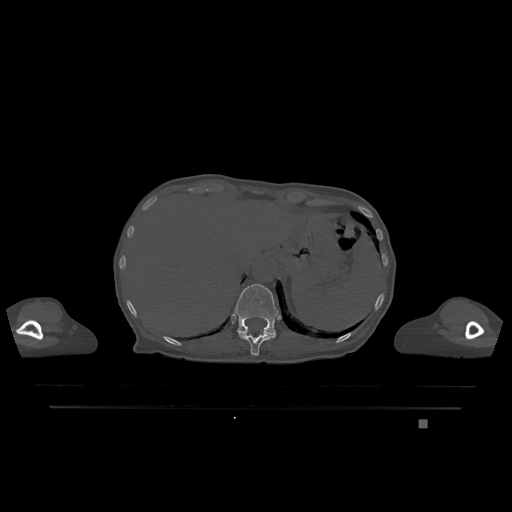
CT including the spine, one axial slice; slice 557 of 1317 in the series (ordered by position); bone window (W 1800 / L 400 HU); 0.5 mm slice thickness; 512 × 512 image matrix, field of view 500 × 500 mm. Female patient, age 74 years. Case-level facts recorded for this patient, not image findings: primary cancer: lung; vertebrae with lytic lesions (as recorded): T1, T4, T5, T6, L4, L5.
Structures marked on this image (semi-automatically segmented with operator editing):
- T11 vertebra: box from (x=238, y=333) to (x=275, y=356) px
- T12 vertebra: (x=234, y=284)–(x=279, y=336)